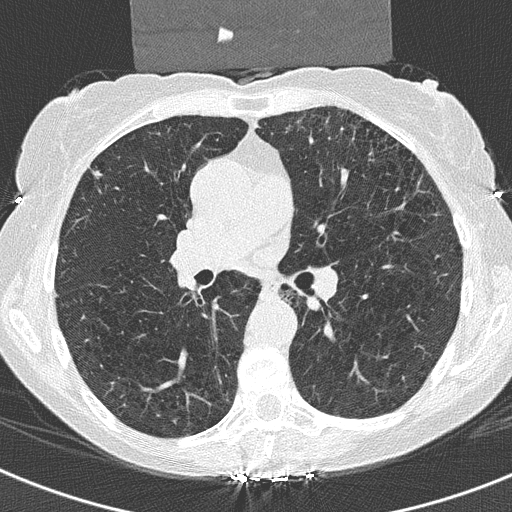
Chest CT (low-dose screening protocol), one axial image. Third screening round (two years after baseline). Lung window (W 1500 / L -600 HU). 2 mm slice thickness. Lung (sharp) reconstruction kernel (B50f). Female participant, aged 70 years at enrolment. Current smoker at enrolment.
• Expert-annotated lung lesion, box from (x=80, y=159) to (x=110, y=191) px.
• Screening reader's record for this exam (one nodule recorded; not confirmed to be the boxed lesion): non-calcified nodule or mass ≥4 mm, right middle lobe, 5 × 5 mm, spiculated (stellate) margins, ground glass attenuation, pre-existing on the prior screen: no.
• Official screen result: positive, other.
• Participant outcome: lung cancer diagnosed 321 days after this screen — adenosquamous carcinoma, right upper lobe, poorly differentiated (G3), stage IA (AJCC 6th edition), 12 mm at pathology.